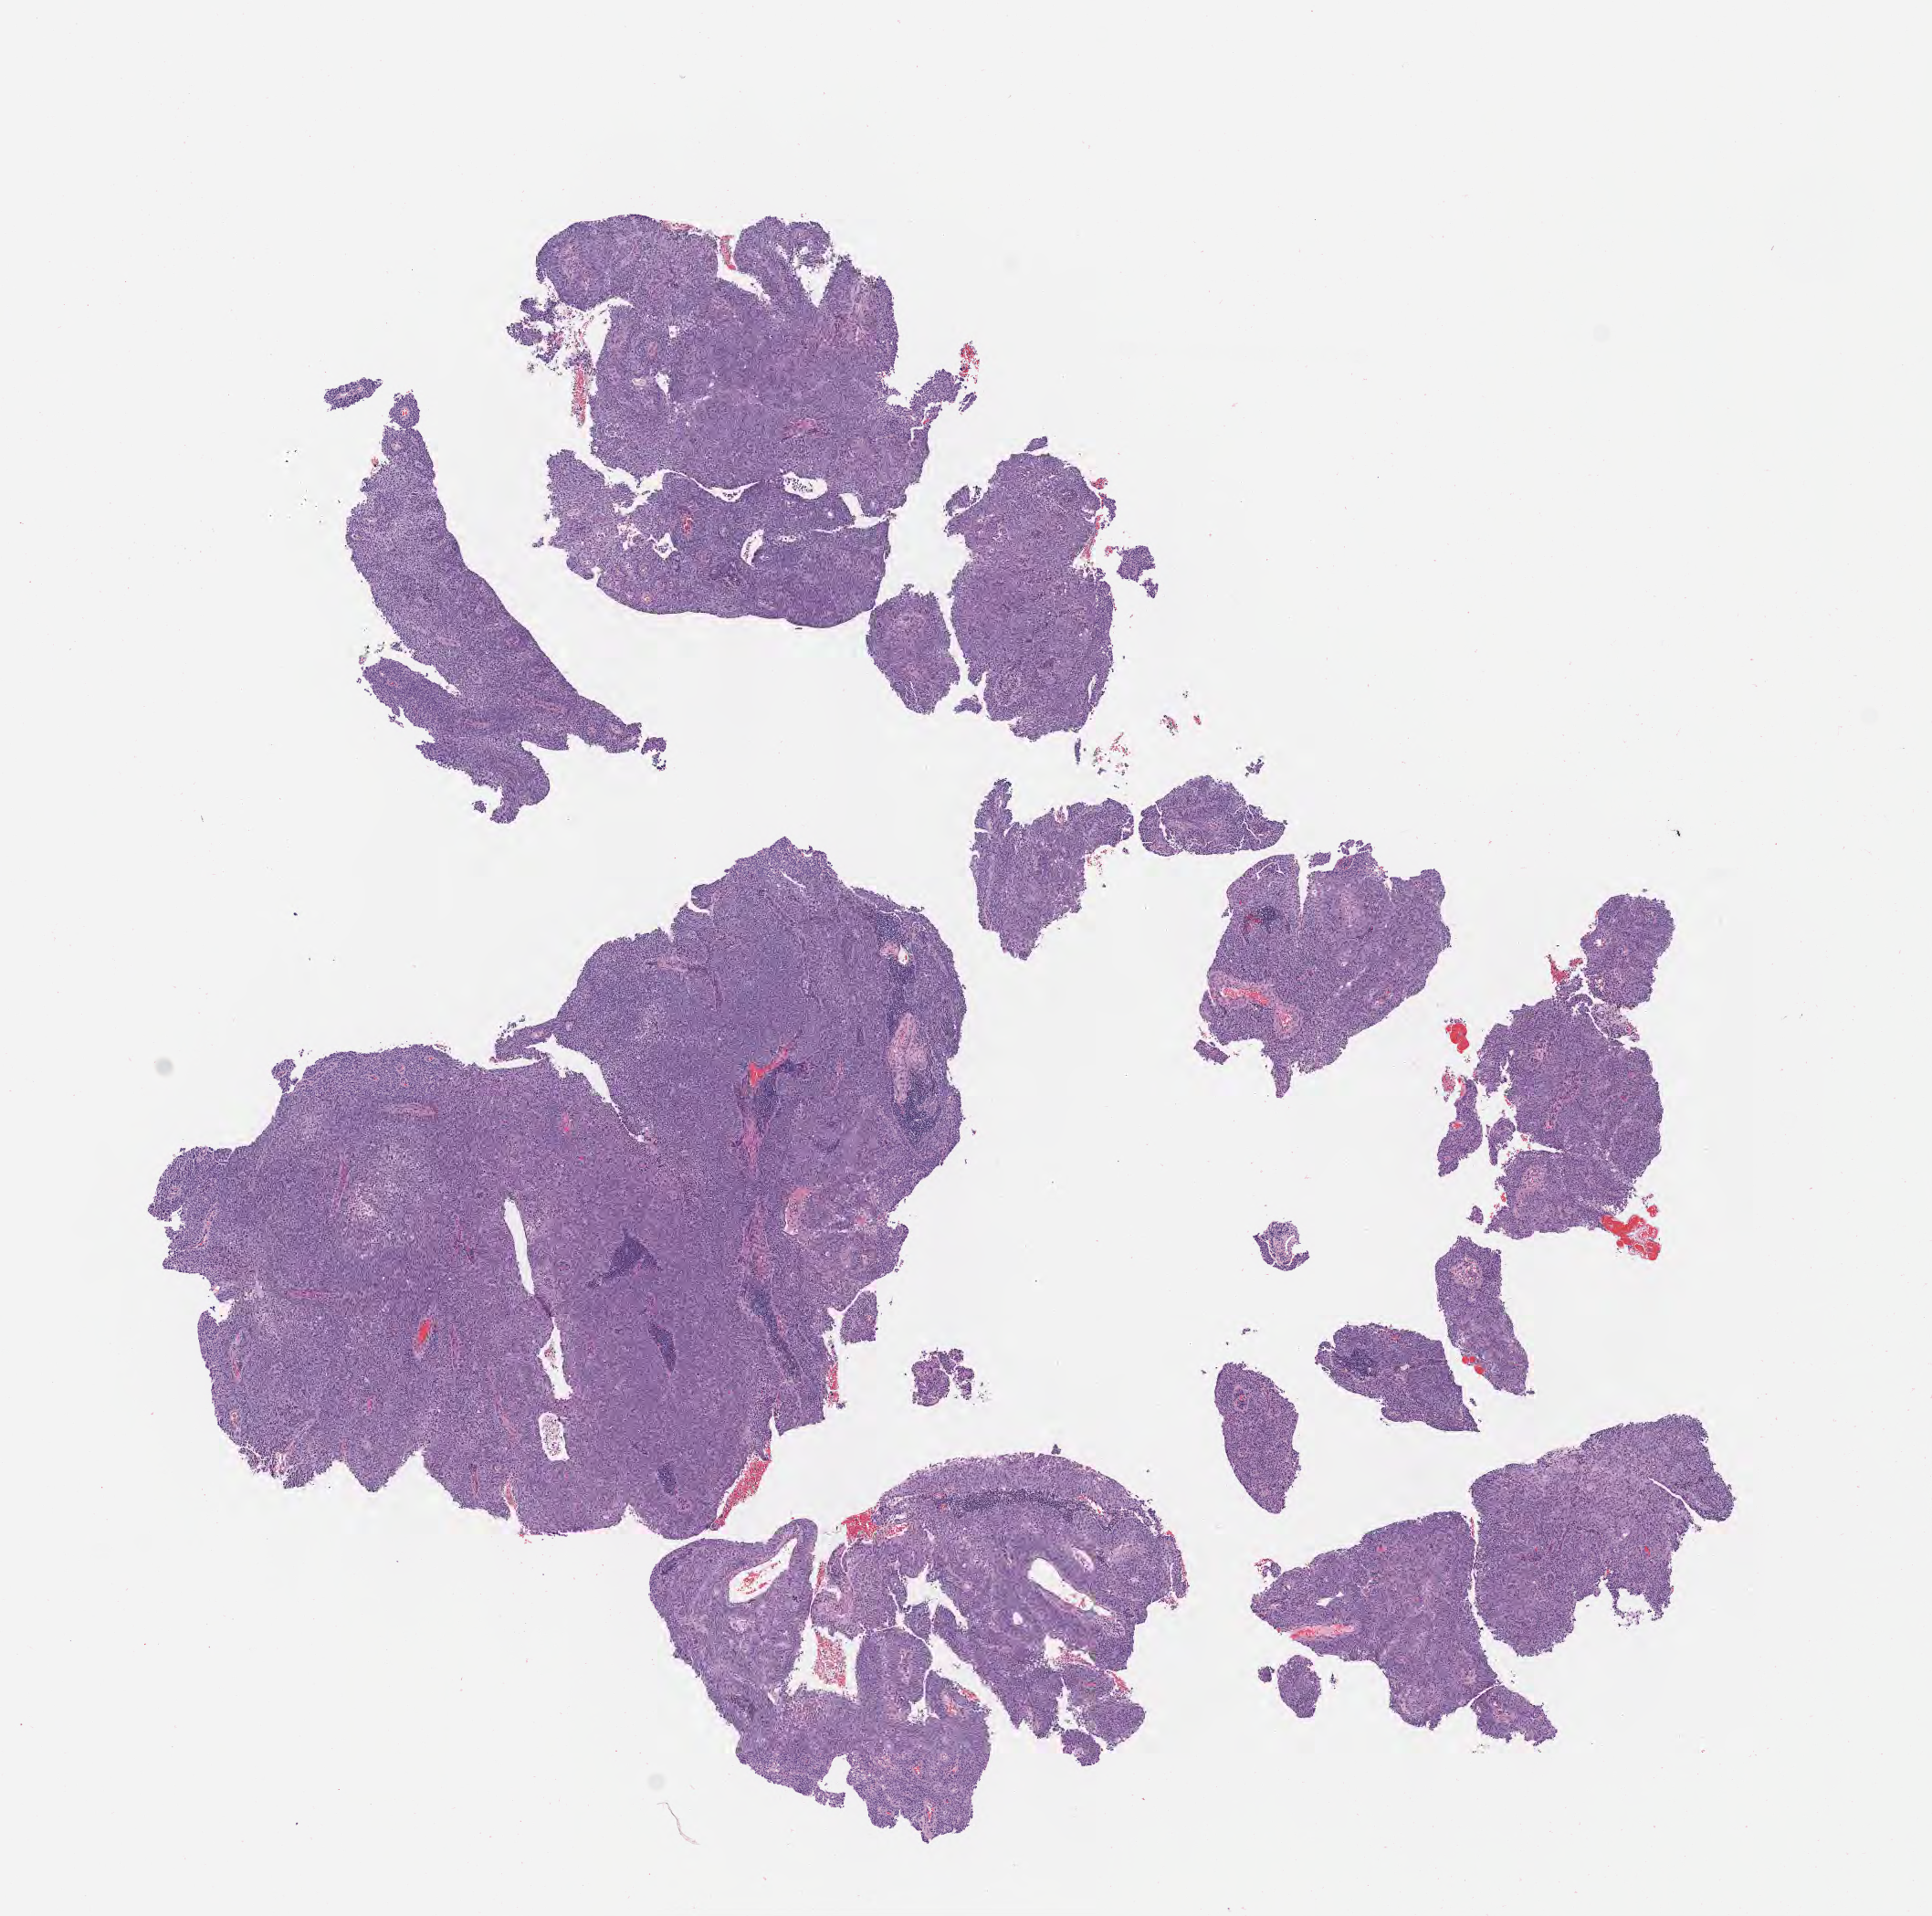
Whole-slide image, H&E stain — low-resolution overview of the scanned area, about 8.6 x 8.5 mm. Specimen: tumor tissue. Anatomic site: cervix. Patient: female, aged 47.
Histologic diagnosis: Squamous cell carcinoma, keratinizing, NOS.